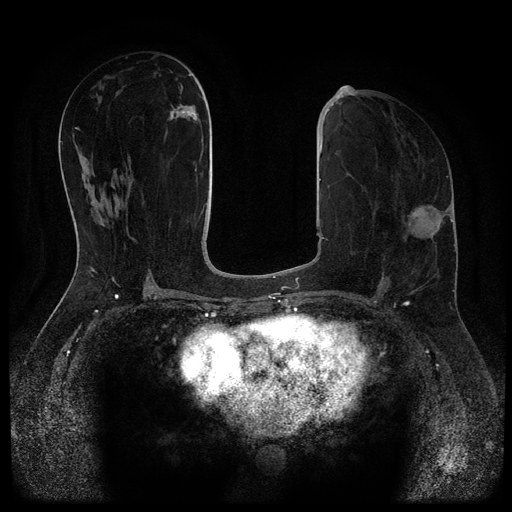
Breast MRI (dynamic contrast-enhanced, multi-phase), one axial slice; slice 48 of 116 in the series (ordered by position); dynamic contrast-enhanced series, time point 2 of 5 at this slice position (early post-contrast); 1.5 T; TE 2.7 ms, TR 5.4 ms; 2 mm slice thickness; 512 × 512 image matrix. Patient: female, 58 years.
Structures marked on this image (semi-automatically segmented with operator editing):
- breast lesion (labelled benign in the annotation): bounding box <168,104,198,121> (left, top, right, bottom; pixels)